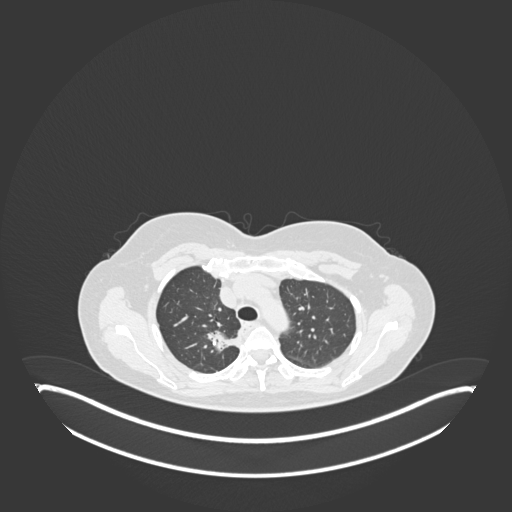
Chest CT, one axial slice. Position 136 of 181 along the scan axis. Reconstruction kernel B30f. Lung window (W 1500 / L -600 HU). 1 mm slice thickness. 512 × 512 image matrix, field of view 500 × 500 mm. Female patient, age 65 years. Case-level facts recorded for this patient, not image findings: clinical TNM (as recorded): T1b N0 M0; histopathological grade: G2.
Annotated regions visible in this slice (rectangle marked by the reading radiologist):
- lung tumour (recorded histology: adenocarcinoma): bounding box (x1, y1, x2, y2) in pixels: (204, 325, 242, 354)